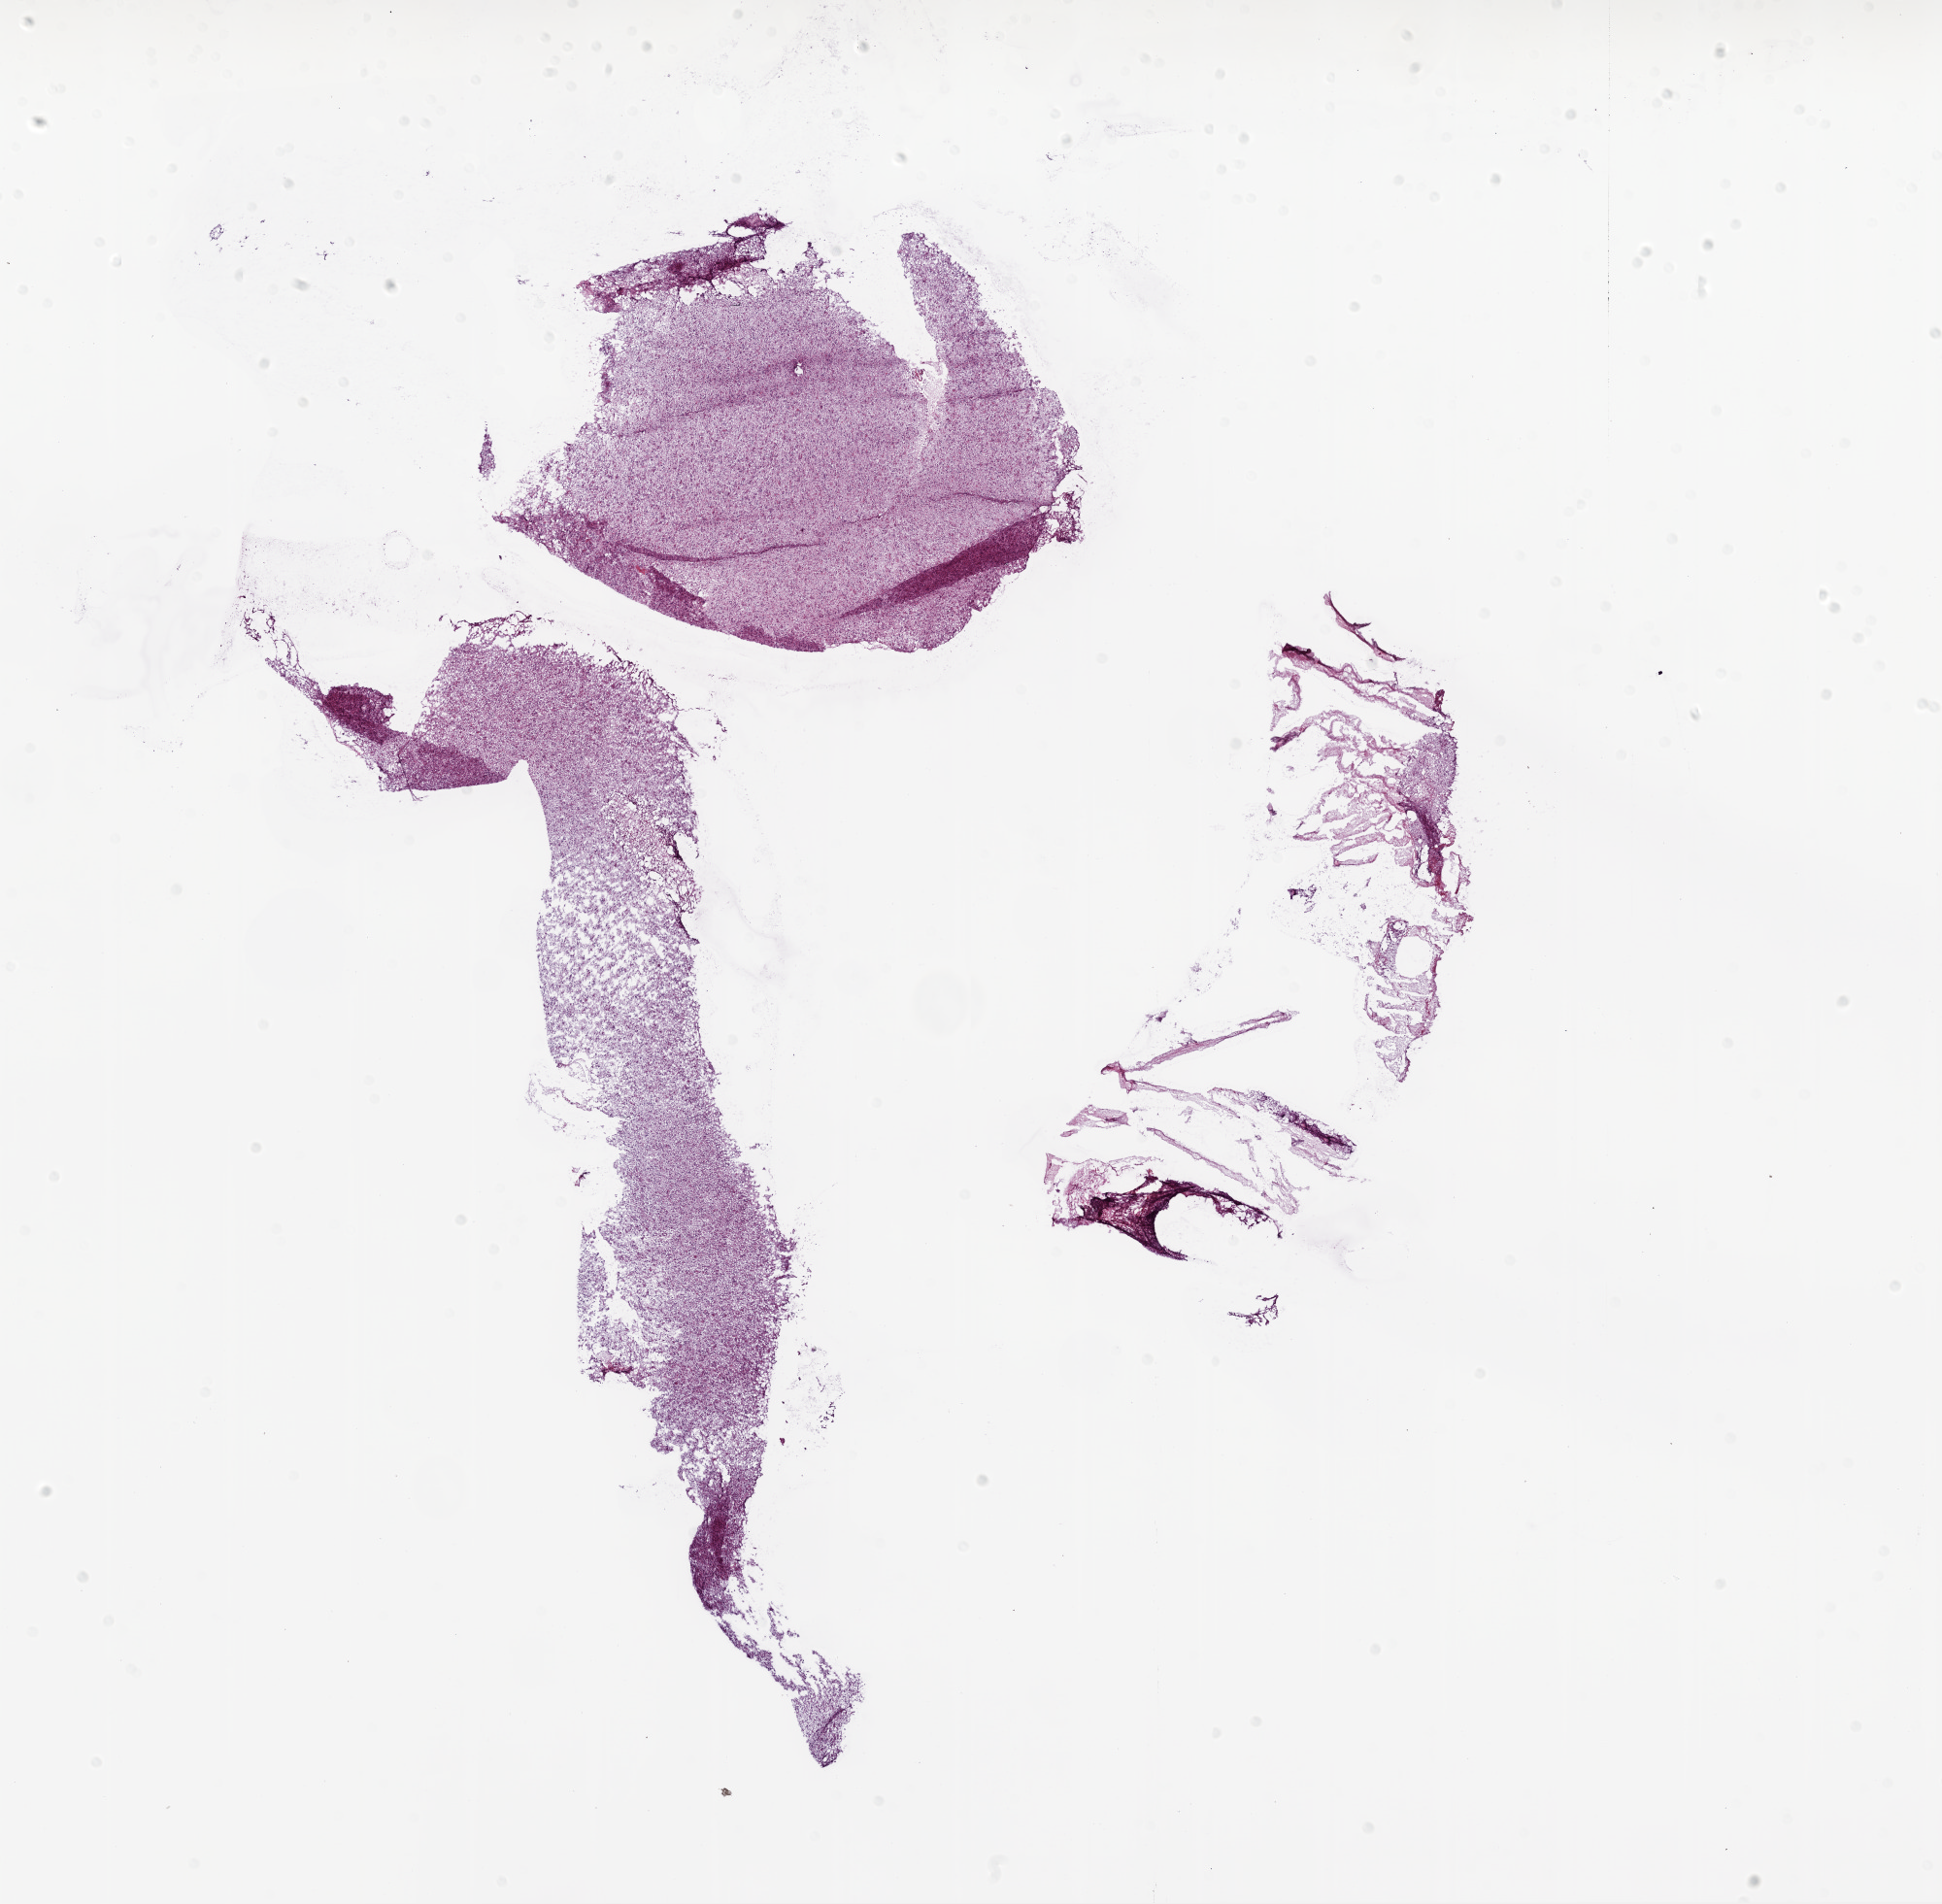
Whole-slide histology image, H&E, shown as a low-resolution overview of the whole scanned area (about 16.0 x 15.7 mm), frozen section from the bottom of the tissue portion, primary tumour sample from the brain. Patient: male, age at initial diagnosis 51 years. Pathologist review of this section (percent, as recorded): tumour cells 90%, tumour nuclei 80%, normal cells 0%, stromal cells 2%, necrosis 8%.
Histologic diagnosis: Glioblastoma.